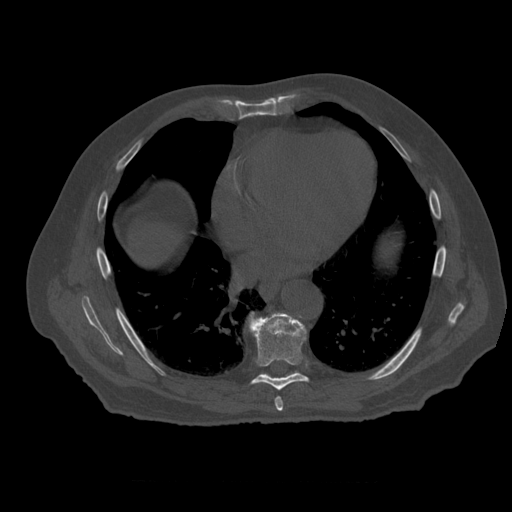
CT including the spine, one axial slice. Slice 340 of 399 in the series (ordered by position). Reconstruction kernel STANDARD. 120 kVp. Bone window (W 1800 / L 400 HU). 512 × 512 image matrix. Patient age 73 years. From the clinical record (not read from this slice): primary cancer: prostate; vertebrae with lytic lesions (as recorded): L2.
Annotated regions visible in this slice (semi-automatic segmentation, software-assisted and operator-edited):
- T7 vertebra: bounding box [x1, y1, x2, y2] px = [275, 397, 283, 413]
- T8 vertebra: [248, 312, 309, 391]
- T9 vertebra: [251, 313, 297, 378]